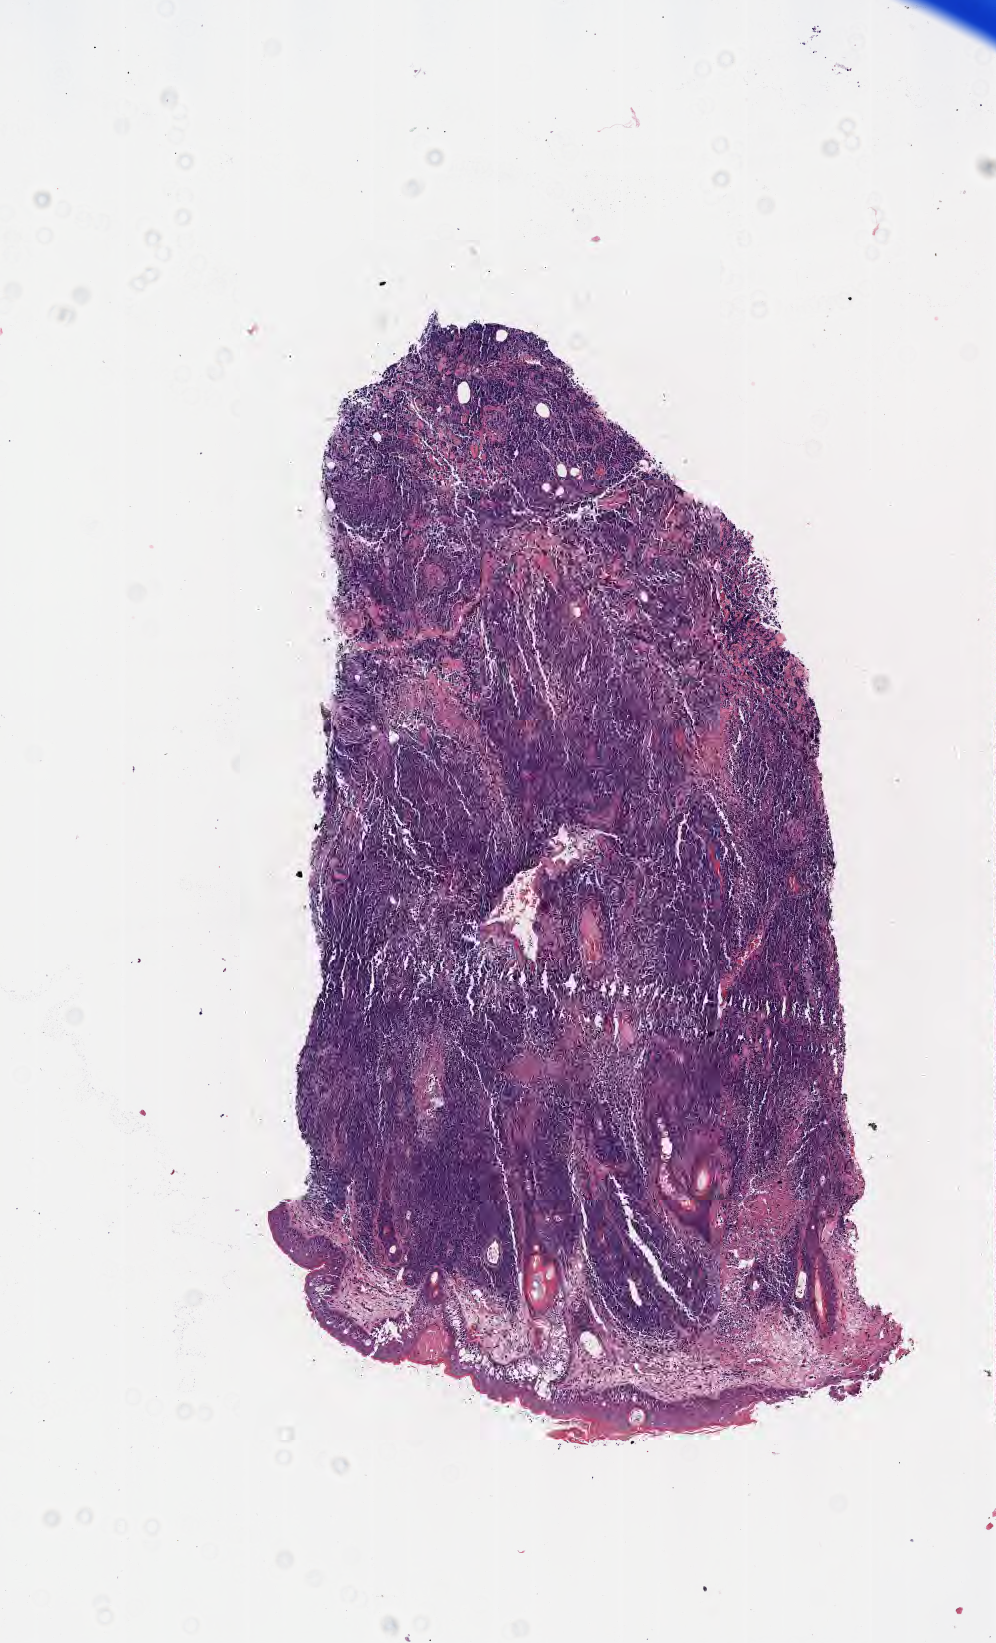
H&E whole-slide image — a low-resolution overview of the entire scanned area, about 4.0 x 6.6 mm, tumor tissue. Patient: male, 41 years old.
Histologic diagnosis: Diffuse large B-cell lymphoma, NOS.